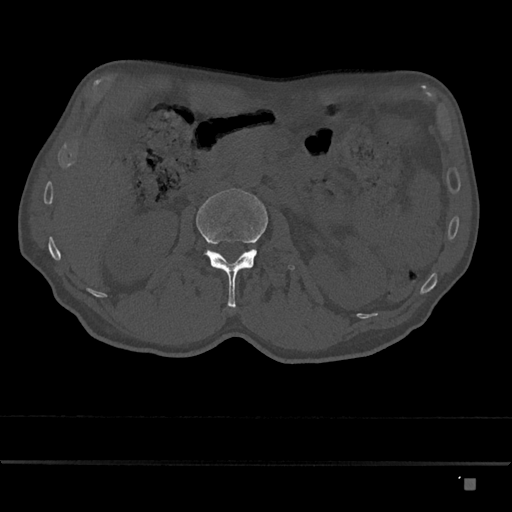
CT including the spine, one axial slice. Position 472 of 797 along the scan axis. Reconstruction kernel Br40s/3. 120 kVp. Bone window (W 1800 / L 400 HU). 0.5 mm slice thickness. 512 × 512 image matrix, field of view 390 × 390 mm. Male patient, age 72 years. Case-level facts recorded for this patient, not image findings: primary cancer: prostate.
Annotated regions visible in this slice (semi-automatically segmented with operator editing):
- L2 vertebra: box from (x=196, y=189) to (x=295, y=308) px